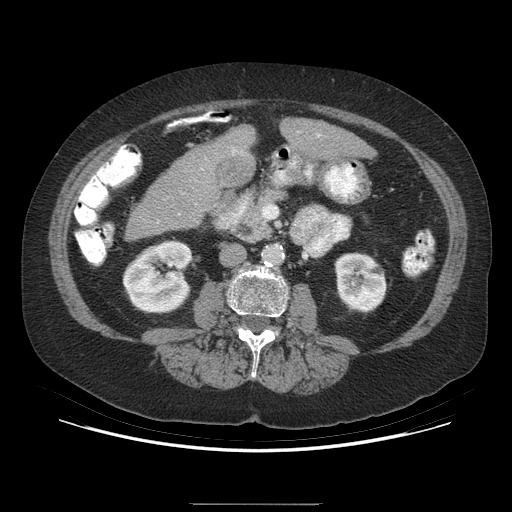
Contrast-enhanced abdominal CT (liver protocol), one axial slice; position 131 of 192 along the scan axis; 140 kVp; soft-tissue window (W 400 / L 40 HU); 2.5 mm slice thickness; 512 × 512 image matrix, field of view 400 × 400 mm. From the clinical record (not read from this slice): diagnosis: hepatocellular carcinoma (patient treated with transarterial chemoembolisation; whether this scan precedes or follows treatment is not stated here); TNM stage (as recorded): Stage-I; Child-Pugh class: A; tumour differentiation: moderately differentiated; tumour nodularity: uninodular.
Outlined on this slice (semi-automatic segmentation, software-assisted and operator-edited):
- liver parenchyma outside the tumour (the mass and vessels are separate outlines, so this box may not span the whole liver): box from (x=126, y=120) to (x=356, y=239) px
- mass: (x=215, y=151)–(x=256, y=187)
- liver vessels: (x=234, y=135)–(x=320, y=151)